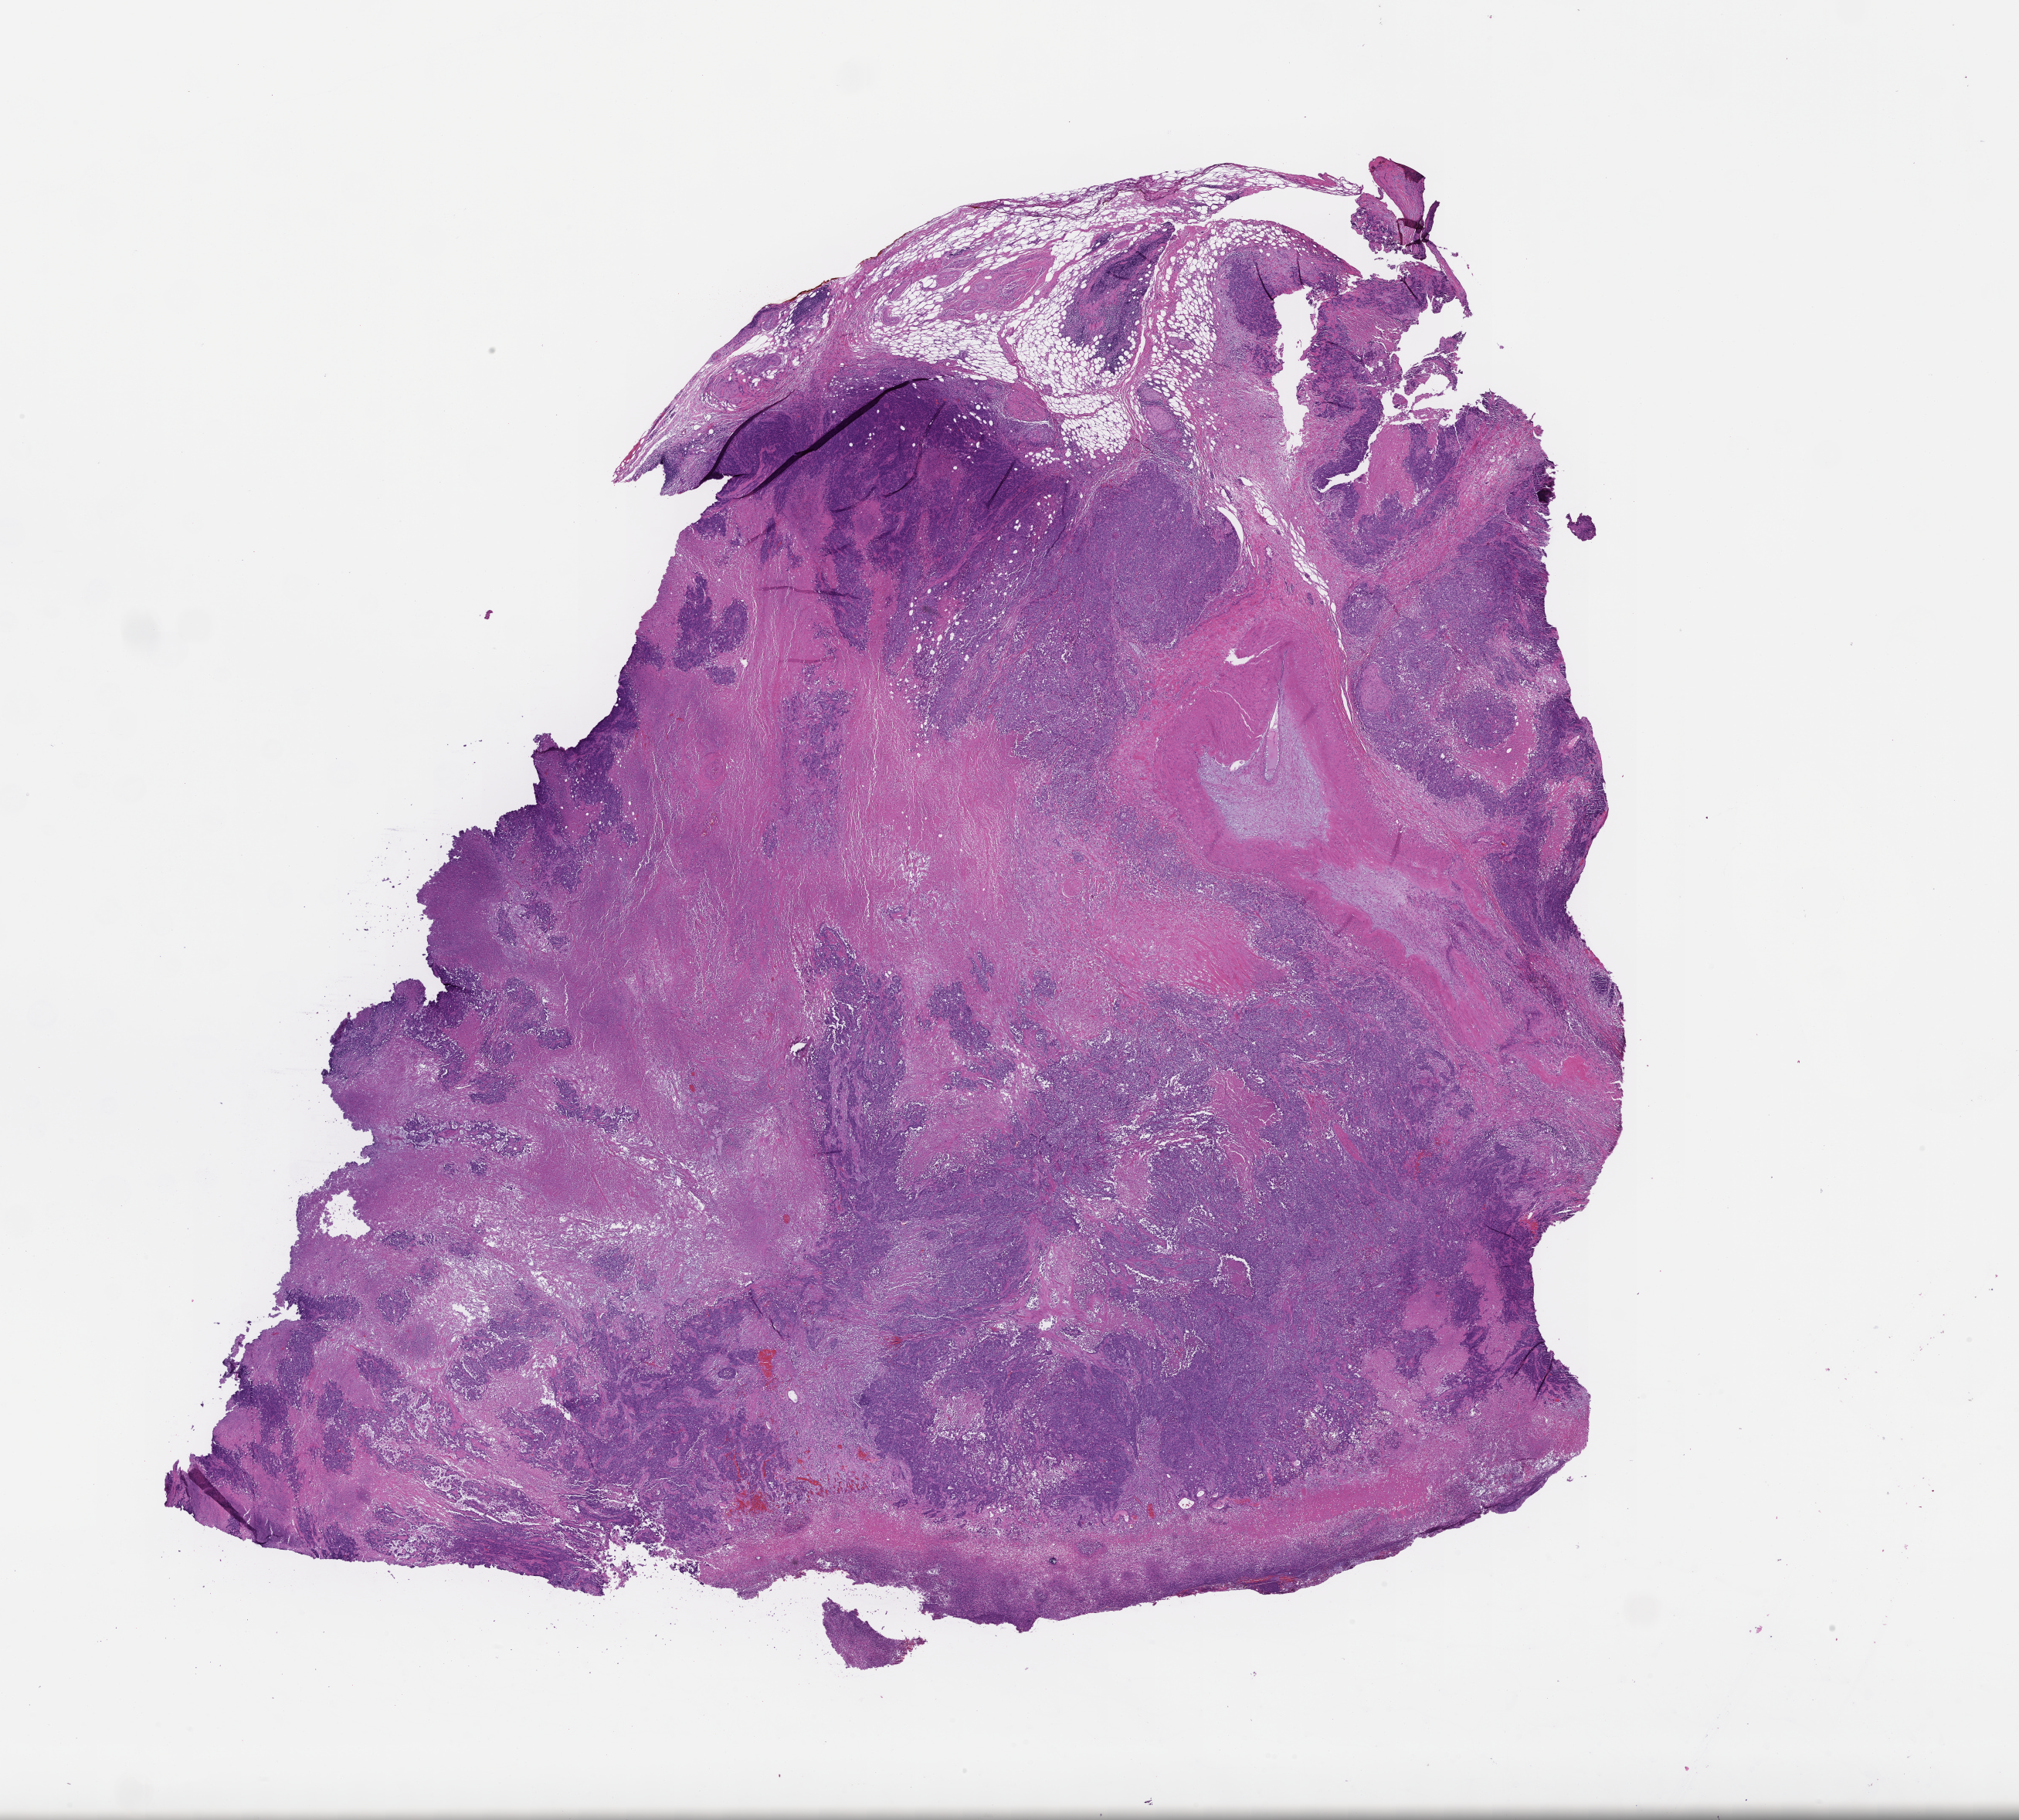
Whole-slide image, H&E stain — low-resolution overview of the scanned area, about 21.1 x 19.0 mm; FFPE section; tissue site: colon. Male patient.
- this section: primary tumour tissue
- diagnosis: Colorectal Carcinoma